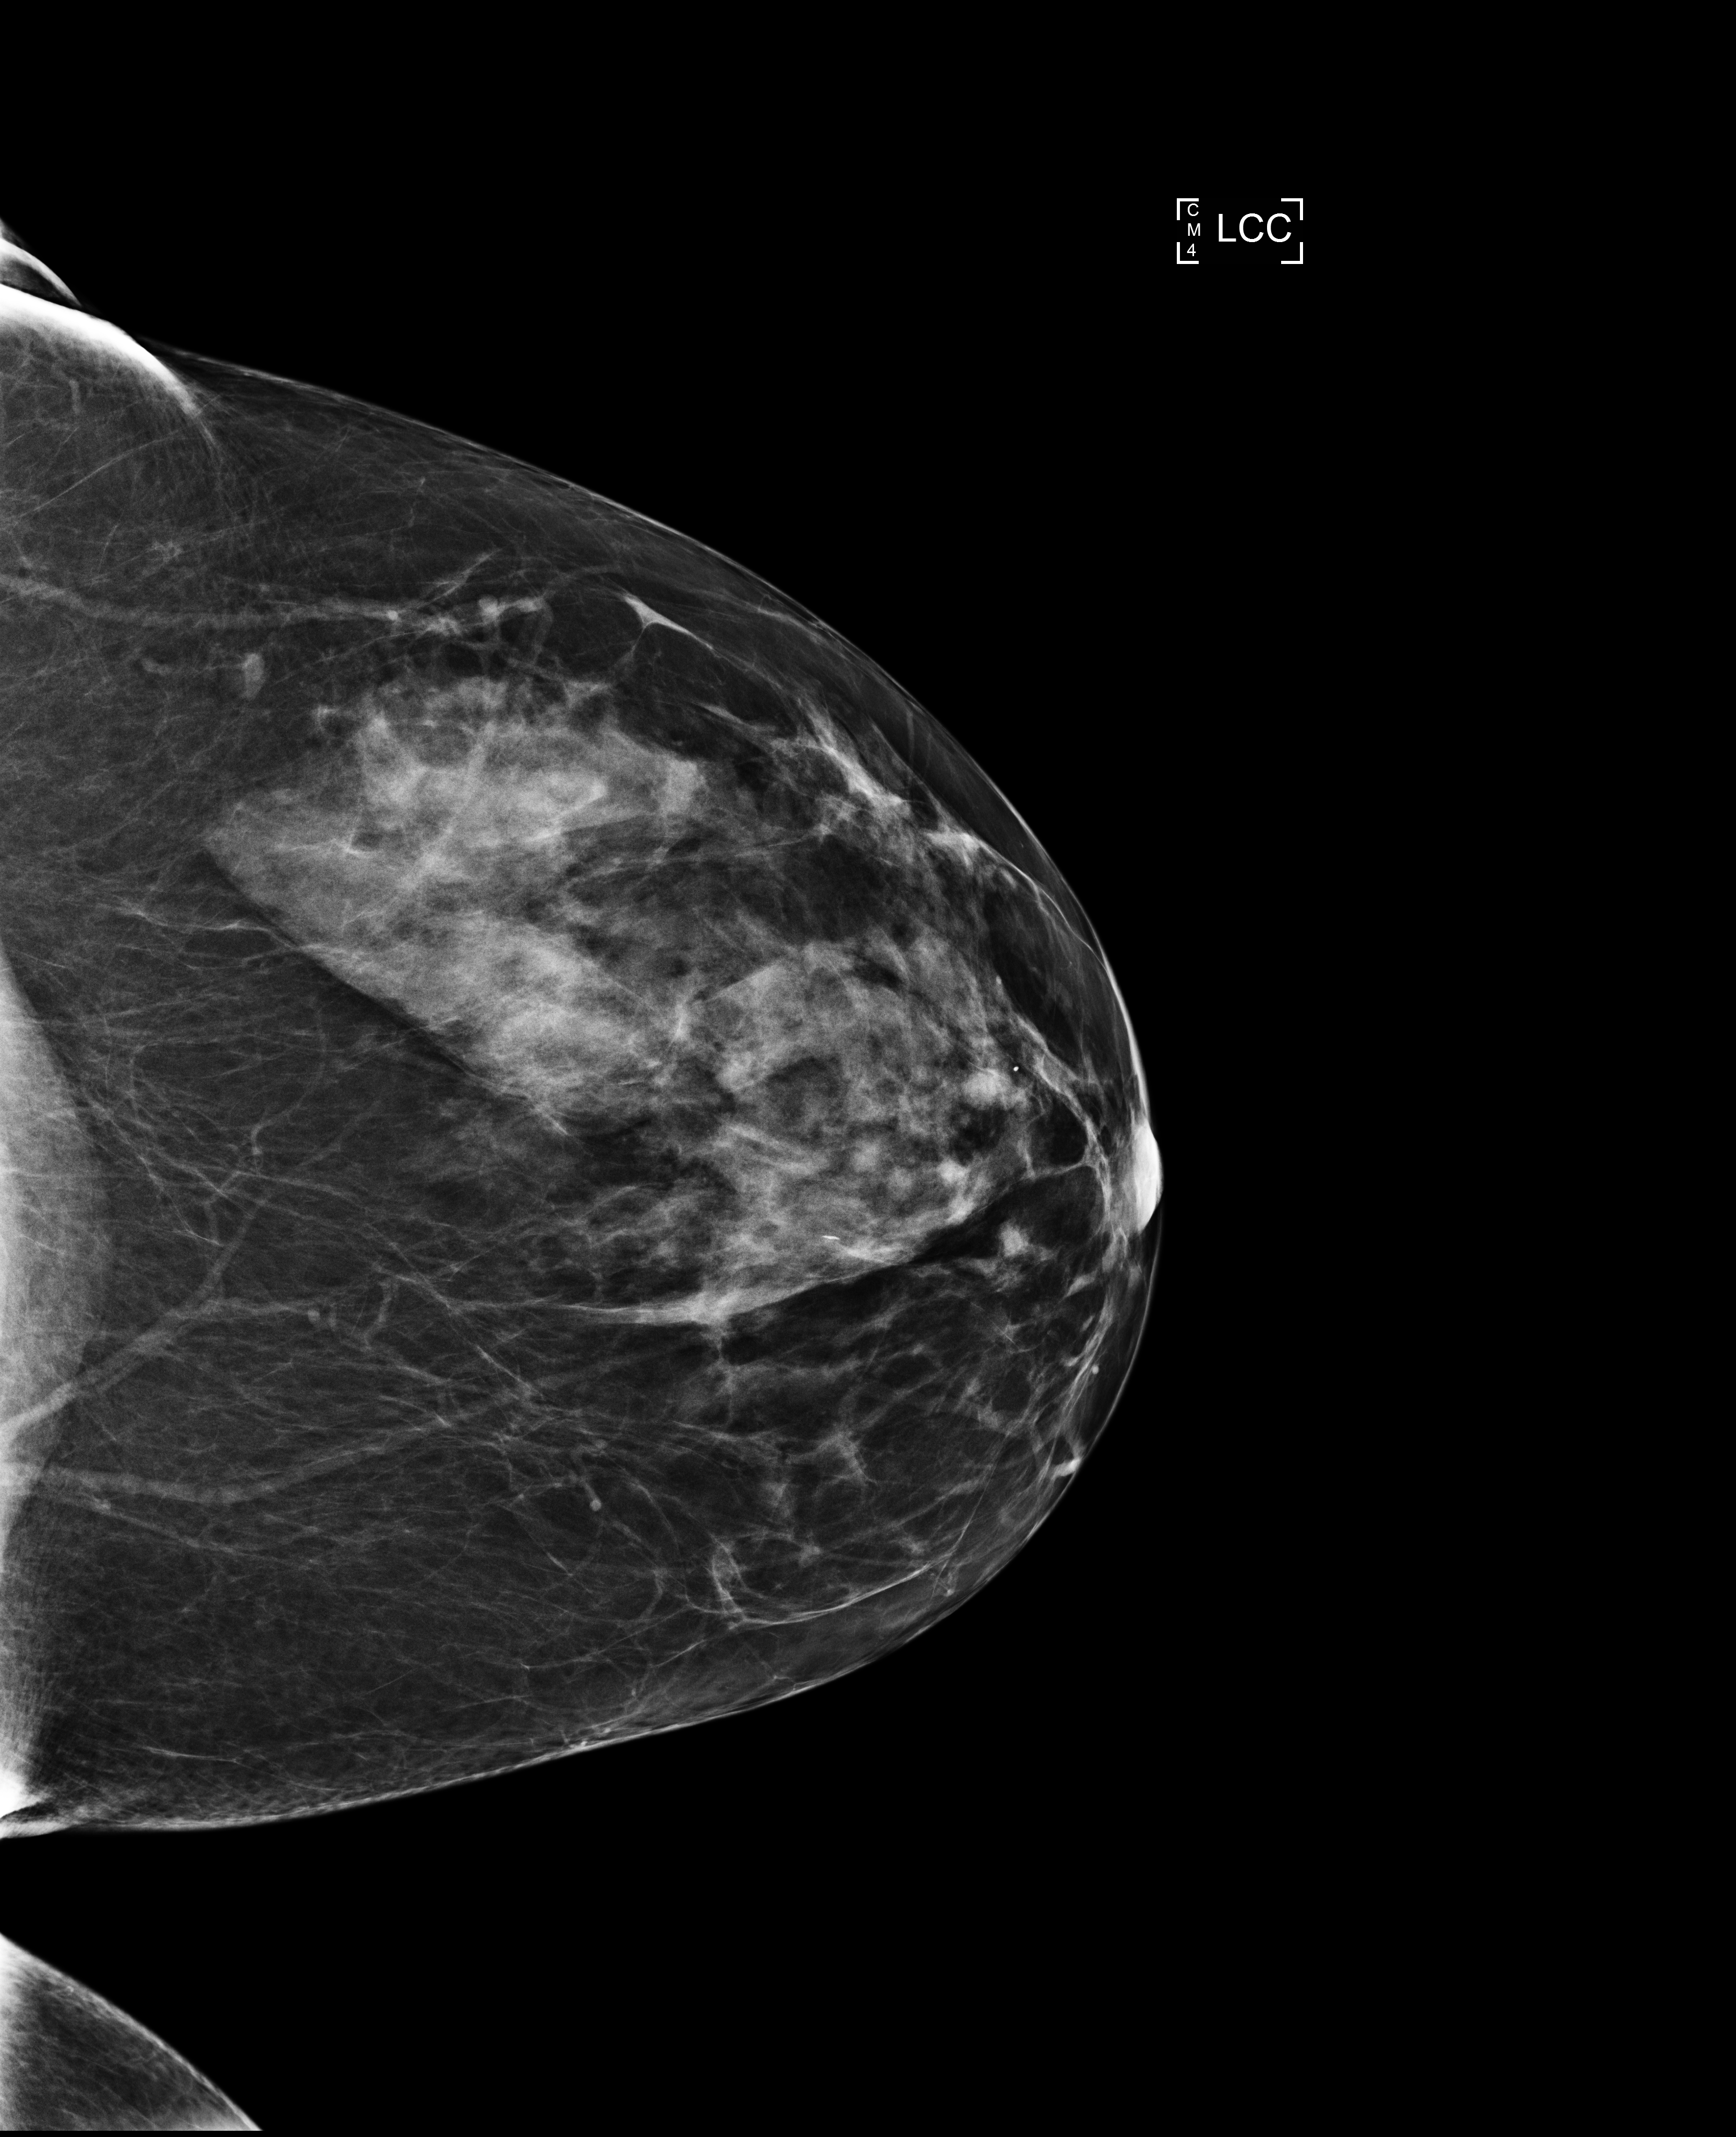
Digital mammogram (FFDM); left breast; craniocaudal (CC) view; annual screening mammography examination. Patient aged 55 years (female).
BI-RADS breast density category at the screening exam (both breasts, scale 1–4): 3. Final BI-RADS assessment for this screening round (tomosynthesis exam, both breasts): category 1. Recall: no recall after this screen.